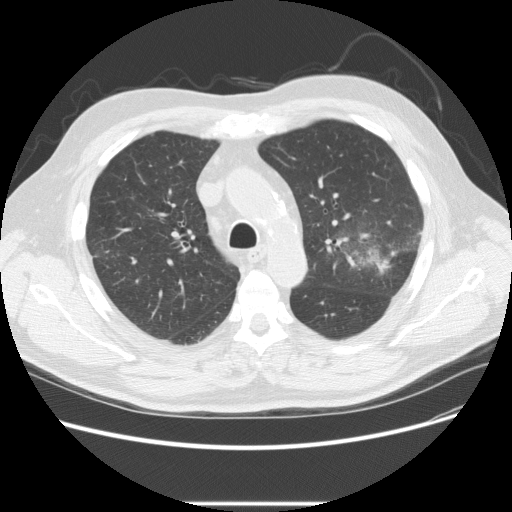
Axial slice from a low-dose chest CT screening exam, baseline screening round, lung window (W 1500 / L -600 HU), 2.5 mm slice thickness, slice 72 of 233 in the series, 512 × 512 image matrix, field of view 380 × 380 mm. Male participant, aged 73 years at enrolment. Former smoker at enrolment.
Expert-annotated lung lesion, bounding box [x1, y1, x2, y2] px = [331, 214, 421, 288]. The screening reader recorded 2 non-calcified nodules or masses ≥4 mm on this exam (left upper lobe, right upper lobe); which of them this box marks is not recorded. Official screen result: positive, change unspecified: nodule(s) >= 4 mm or enlarging nodule(s), mass(es), or other non-specific abnormalities suspicious for lung cancer. Lung cancer was diagnosed 11 days after this screen: bronchiolo-alveolar adenocarcinoma, NOS, other location, well differentiated (G1), stage IV (AJCC 6th edition).